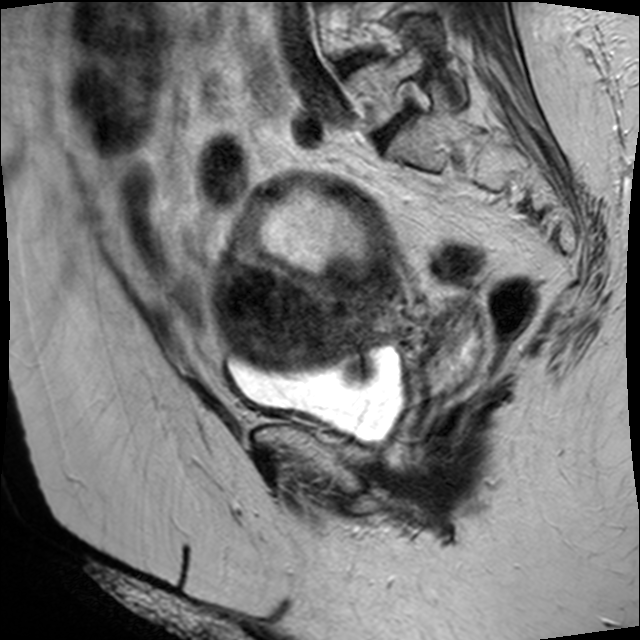
Pelvic MRI for cervical cancer, one sagittal slice. Position 27 of 45 along the scan axis. T2-weighted. 1.5 T. TE 89 ms, TR 4610 ms. 4 mm slice thickness. 640 × 640 image matrix. Female patient, age 50 years.
Outlined on this slice (outlined manually by an expert reader):
- uterus and cervix: bounding box [x1, y1, x2, y2] px = [212, 169, 487, 404]